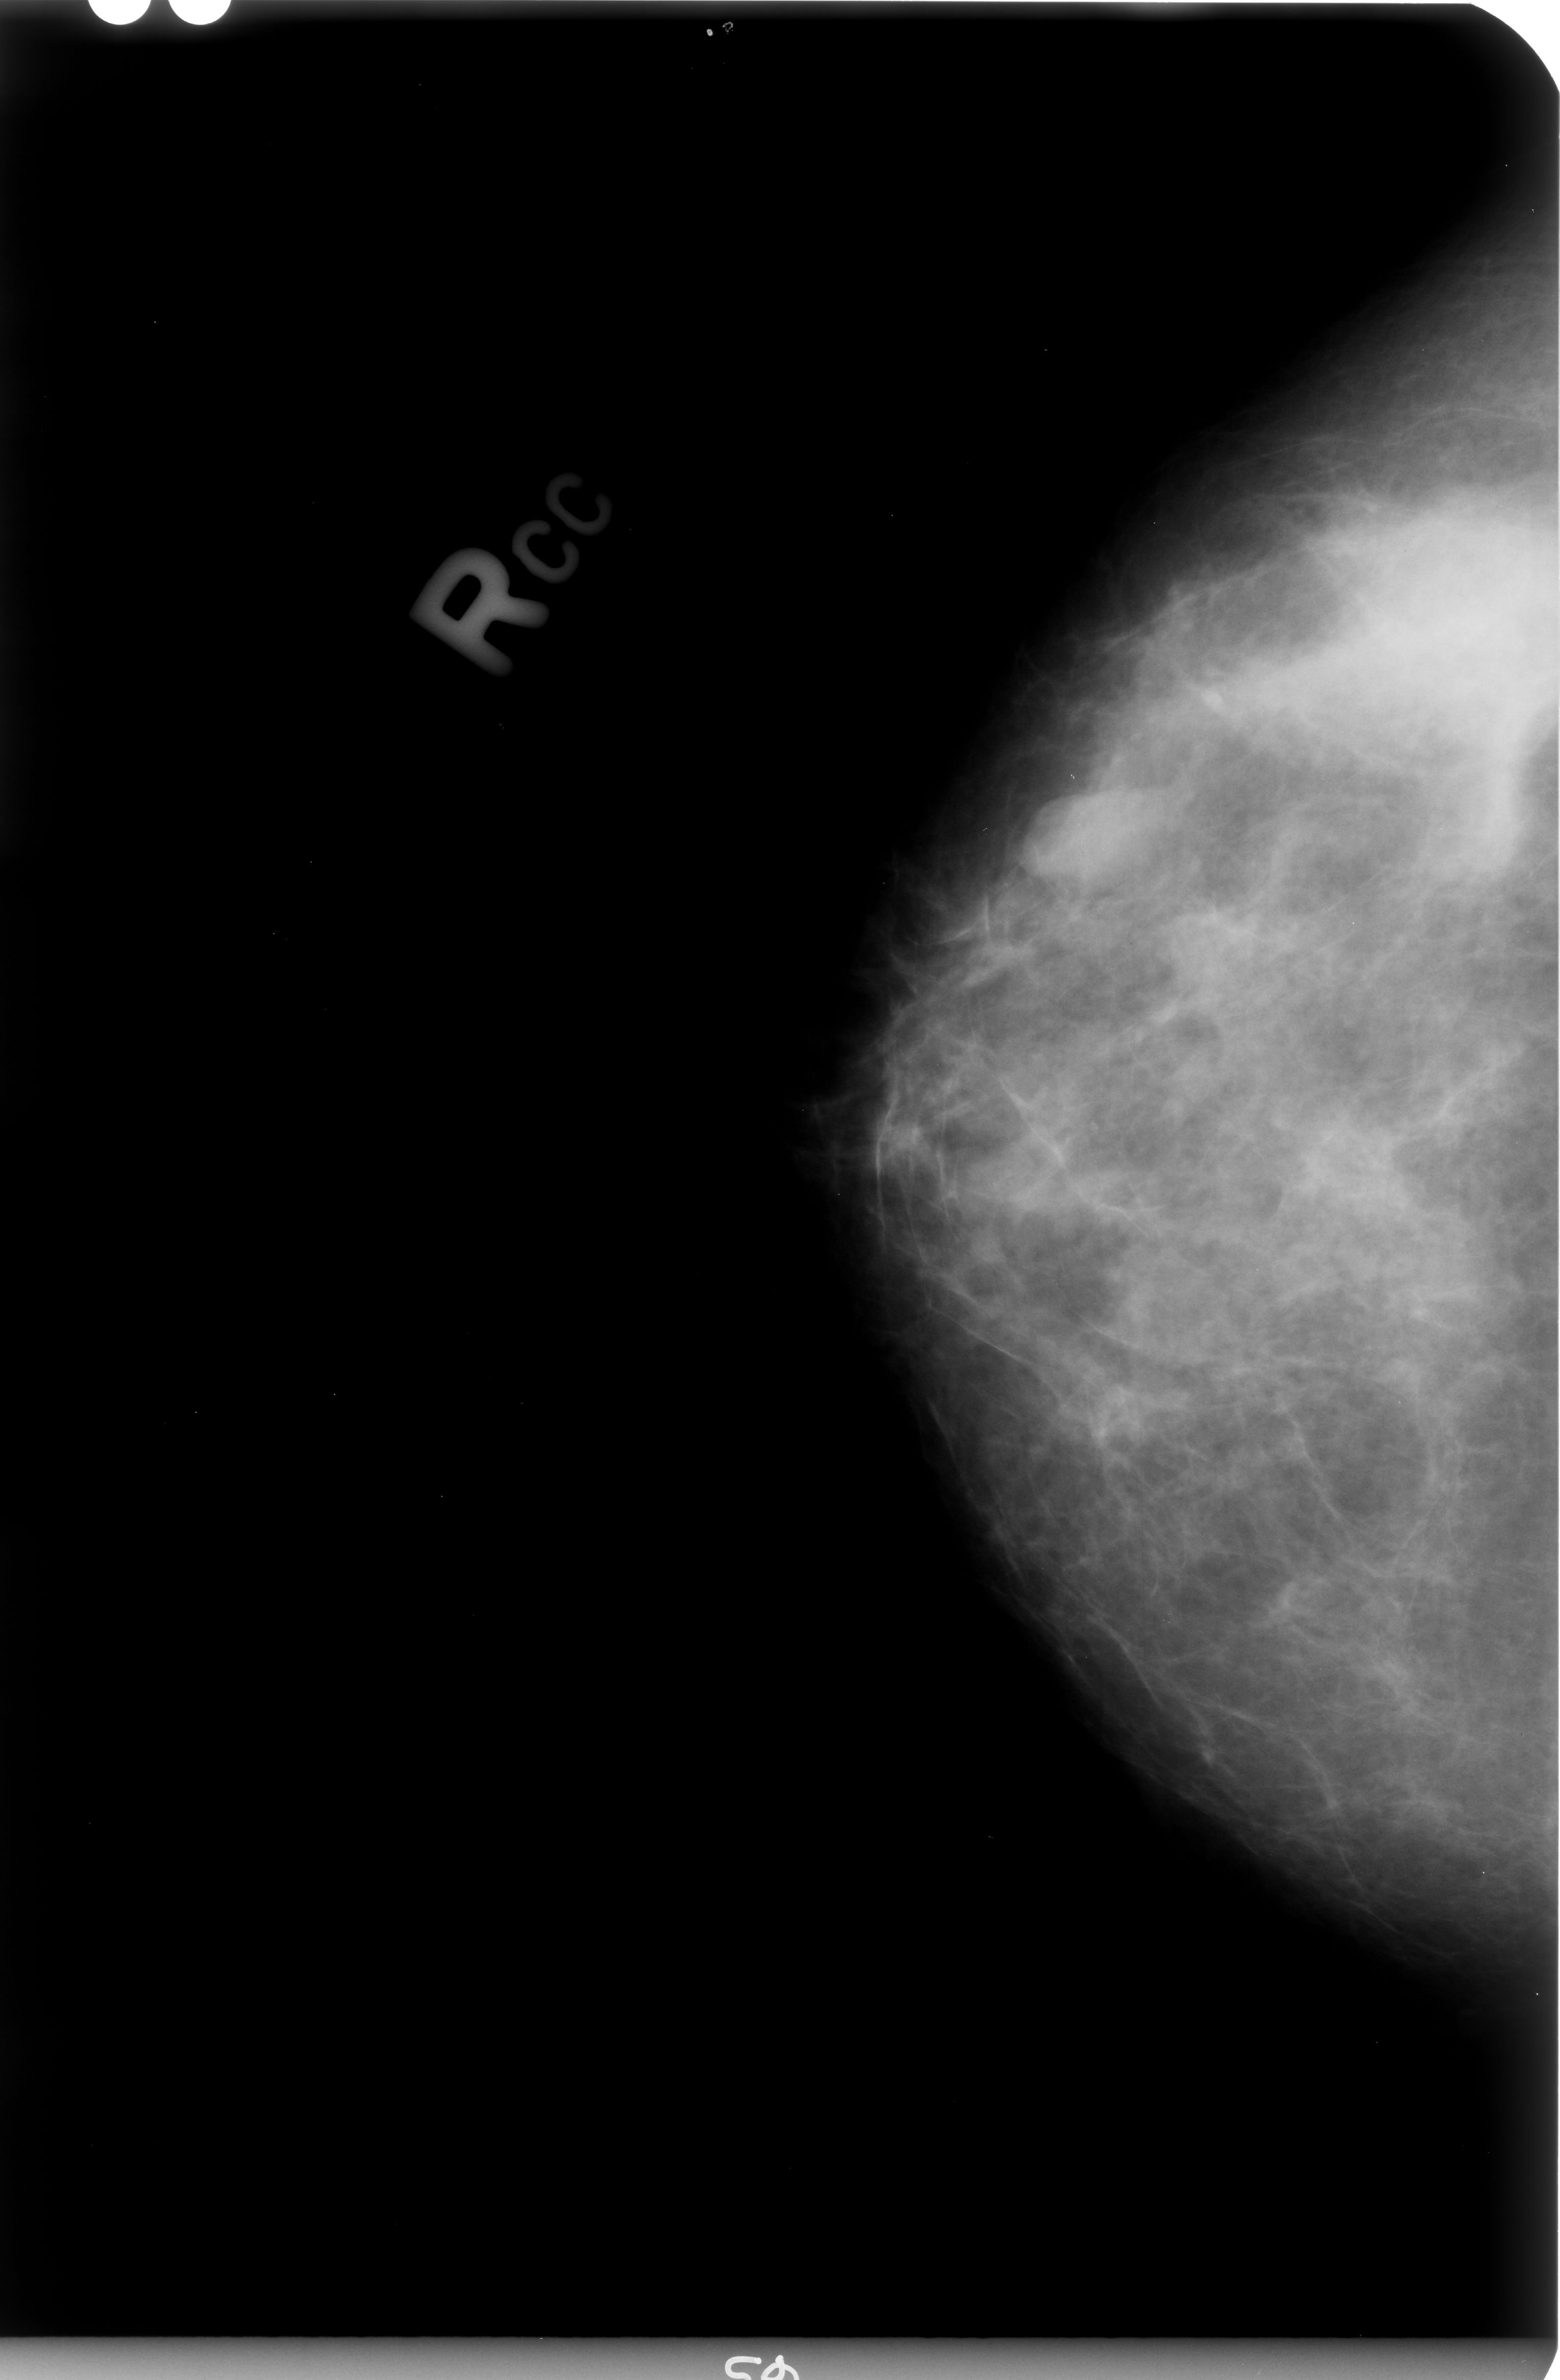
Digitized screen-film mammogram; right breast; craniocaudal (CC) view; BI-RADS breast density category 3 (scale 1–4).
Marked abnormality: mass, shape lobulated, margins circumscribed / ill defined; BI-RADS assessment category 4; pathology result (as recorded, not read from the image): benign.